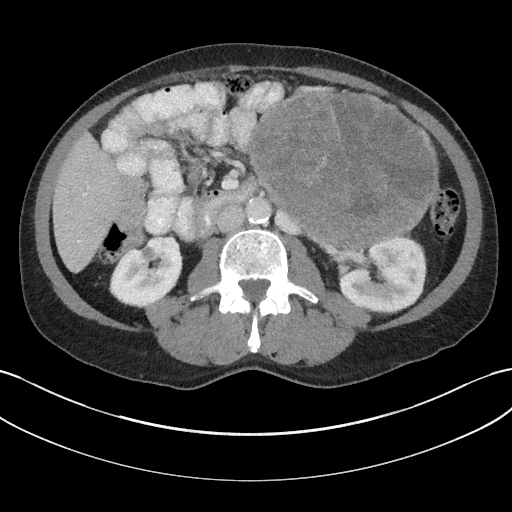
Contrast-enhanced abdominal CT, one axial slice; position 87 of 147 along the scan axis; reconstruction kernel I31f/3; 100 kVp; intravenous contrast given; soft-tissue window (W 400 / L 40 HU); 3 mm slice thickness; 512 × 512 image matrix, field of view 384 × 384 mm. Patient: male, 58 years. Case-level facts recorded for this patient, not image findings: diagnosis: adrenocortical carcinoma; tumour side: left adrenal; tumour size at pathology: 22 cm; Ki-67 index: 26 %; stage (as recorded): 2.
Structures marked on this image (semi-automatically segmented with operator editing):
- mass: bounding box <250,93,437,247> (left, top, right, bottom; pixels)